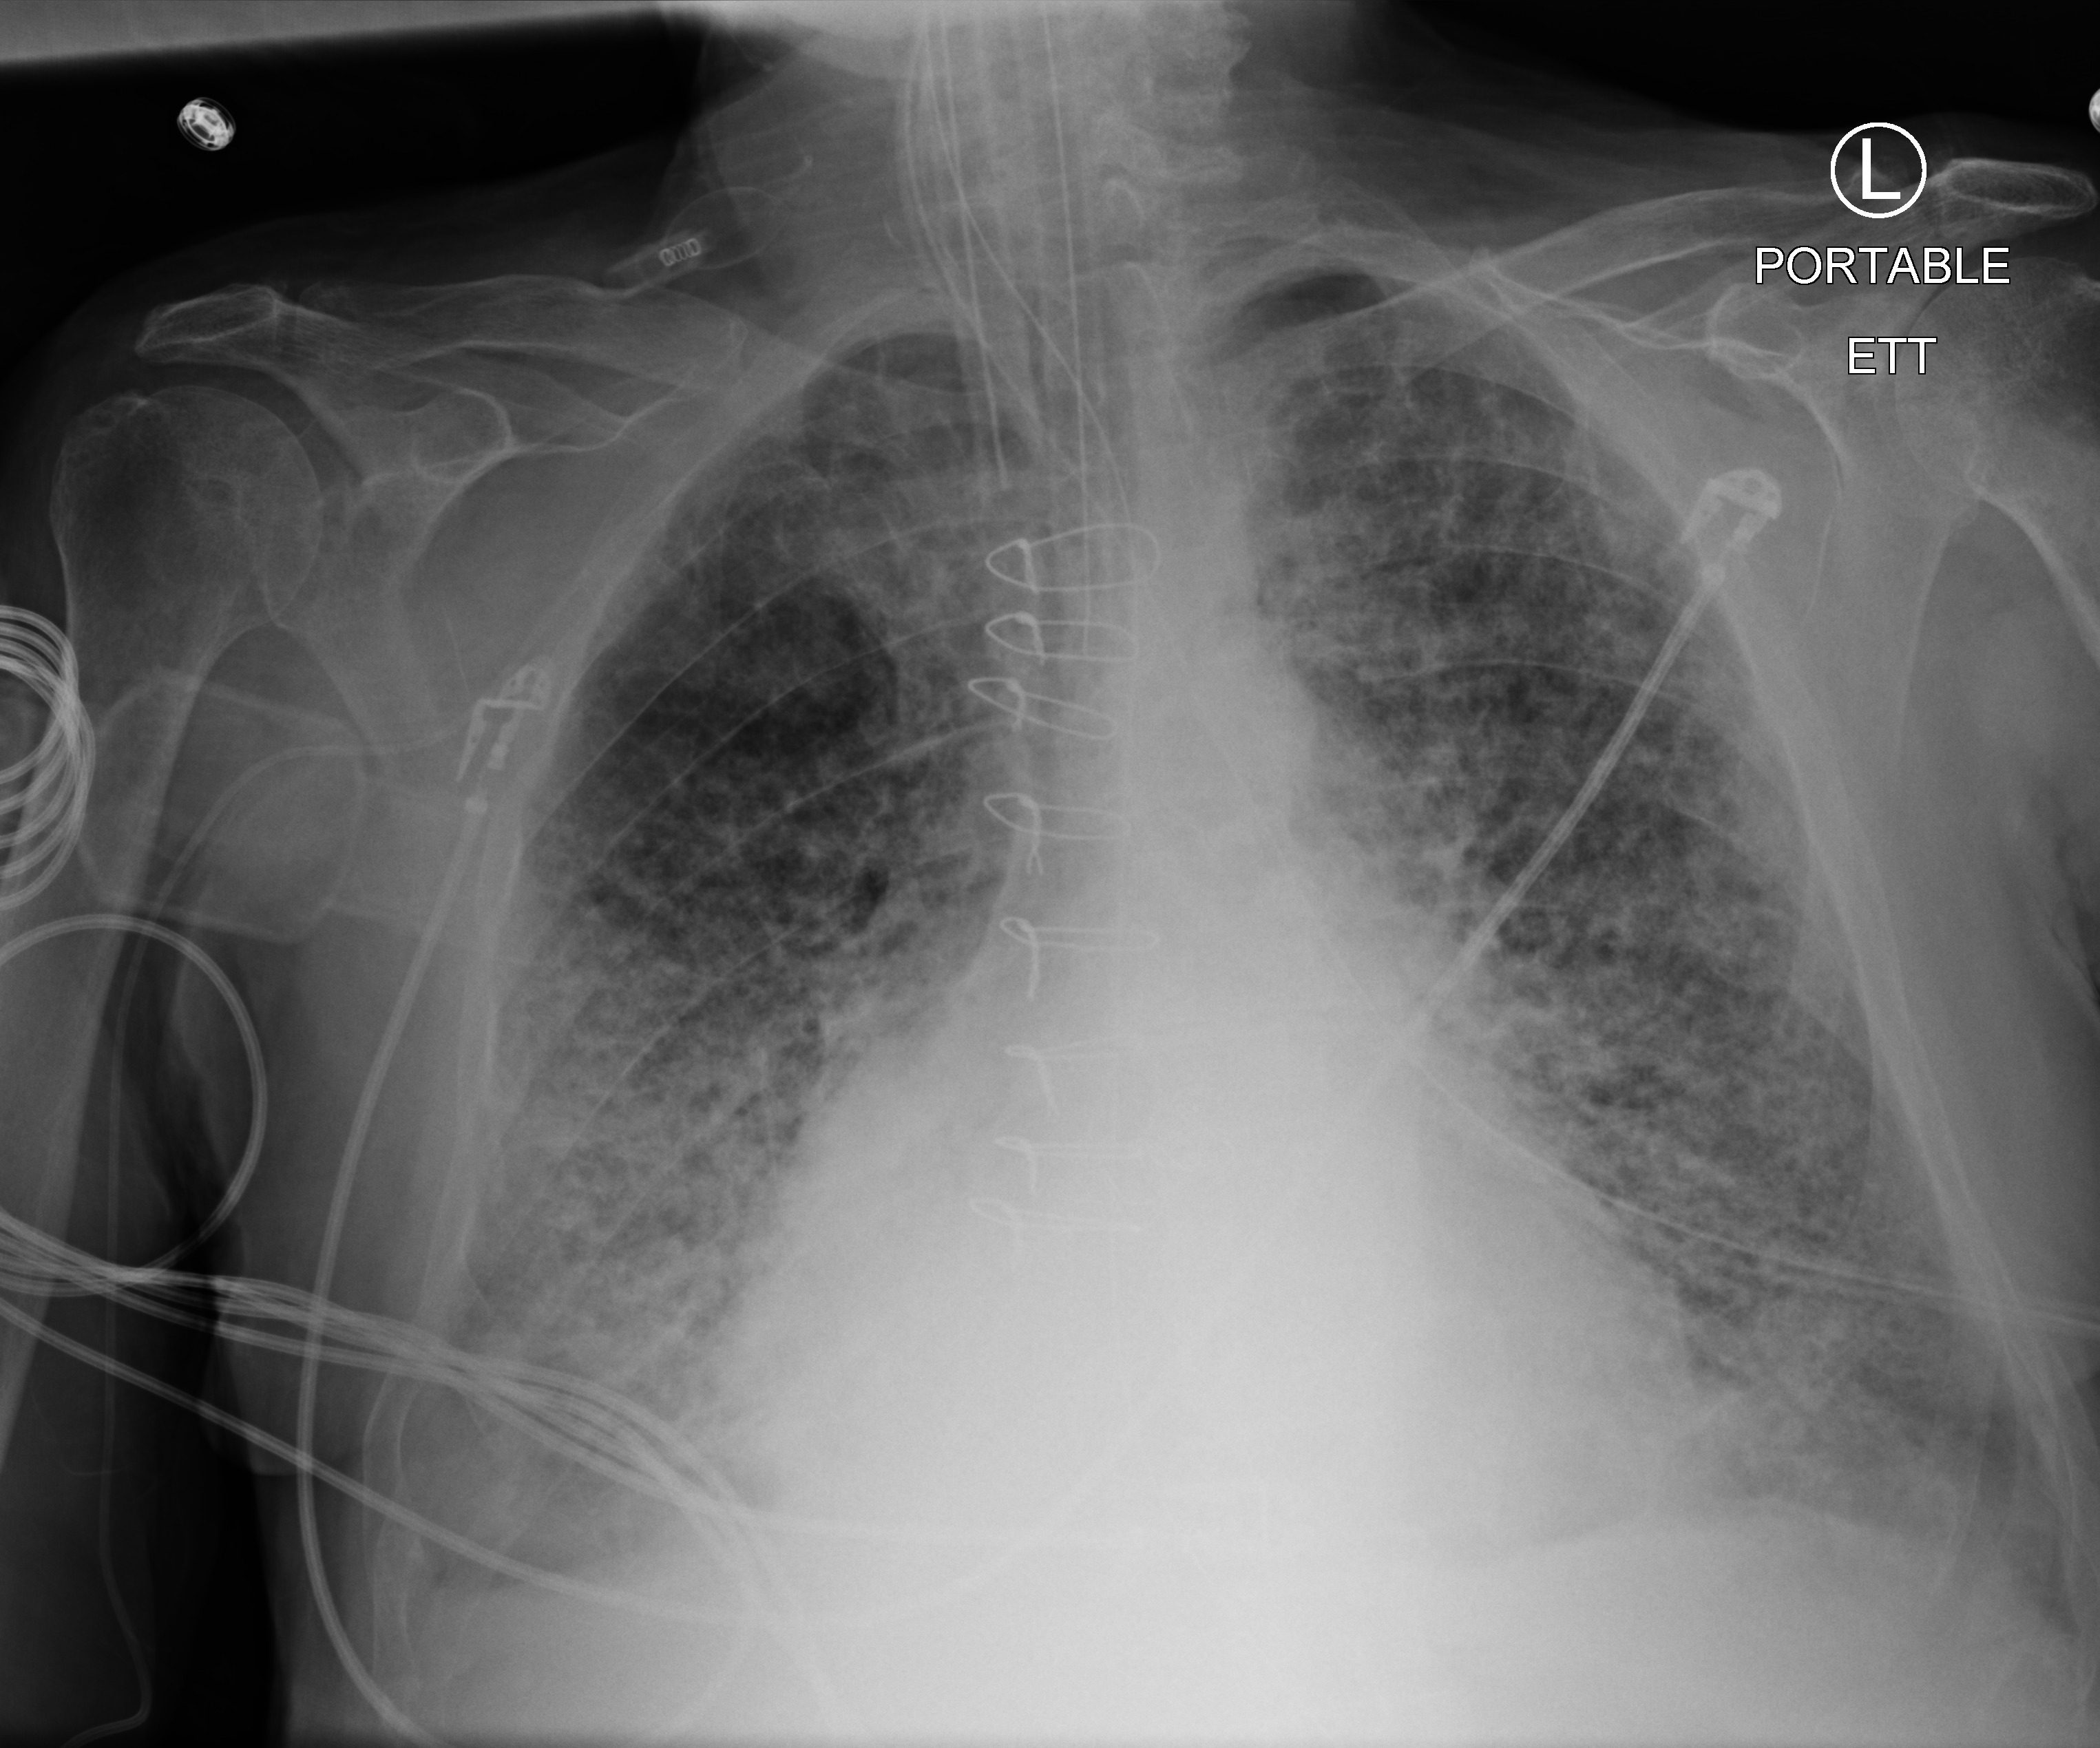
Bedside chest radiograph (computed radiography); anteroposterior (AP) projection. Patient hospitalised with COVID-19; male, aged 75–90 years.
Admission-level facts for this patient (not findings on this image; timing relative to this image not recorded): mechanically ventilated during this hospital stay: yes; length of hospital stay: 40 days; admitted to intensive care during this hospital stay: yes.